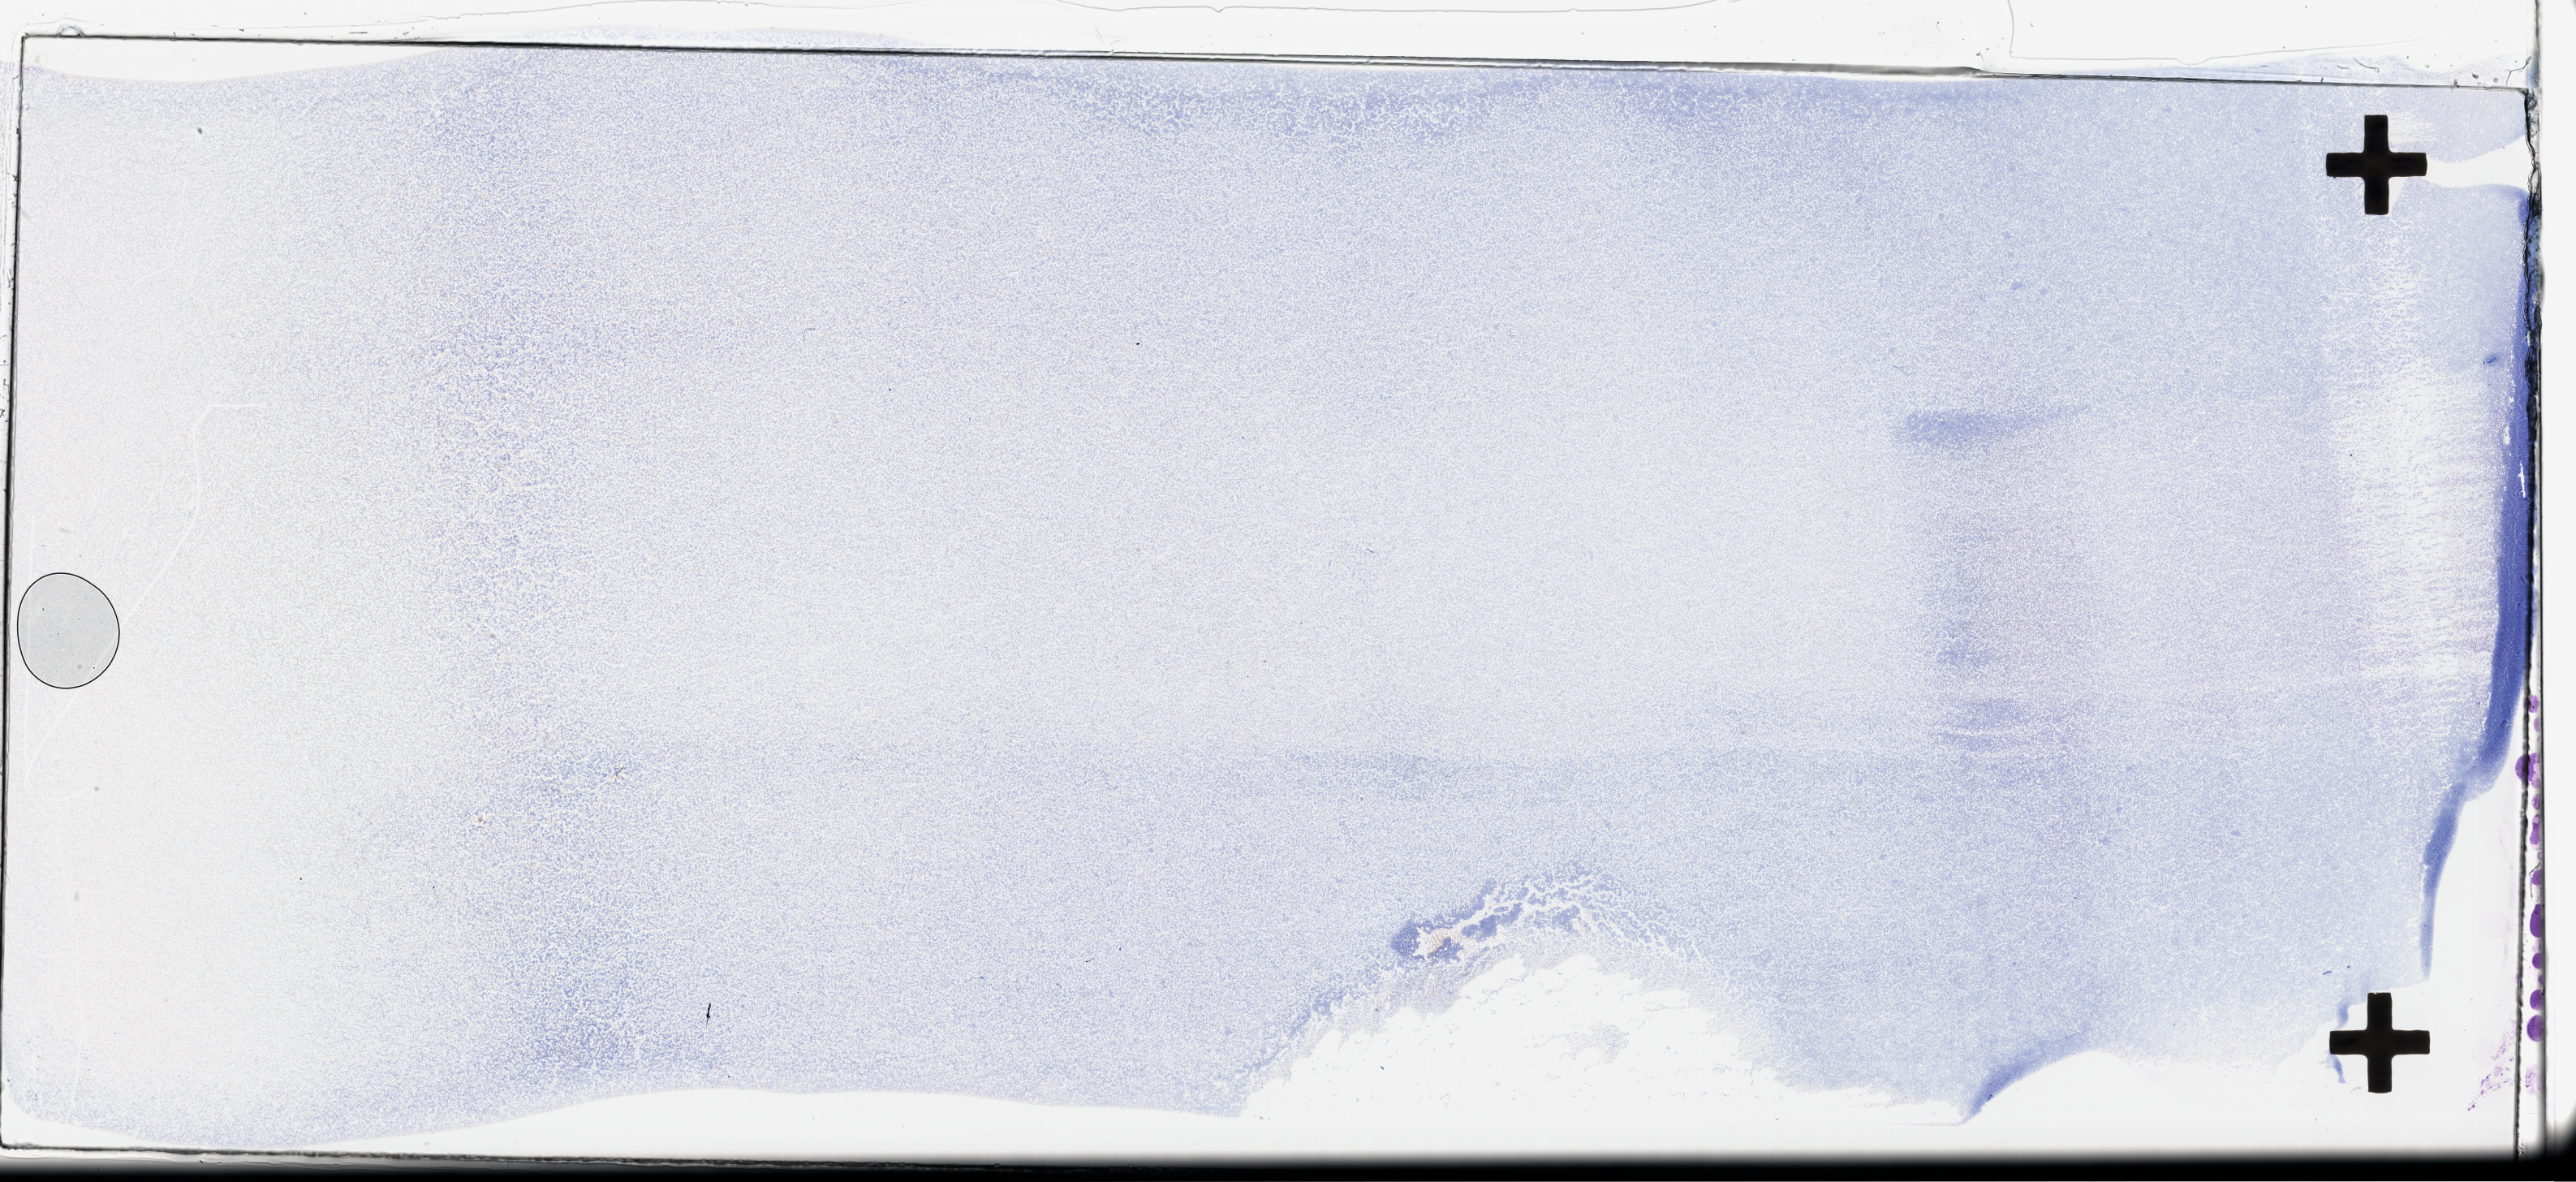
Hematoxylin and eosin (H&E) stained whole-slide image — whole scanned area (about 51.3 x 23.5 mm) shown as a low-resolution overview; peripheral blood (leukaemic) sample. Female, 70 y/o.
• FAB classification: M1
• diagnosis: Acute Myeloid Leukemia